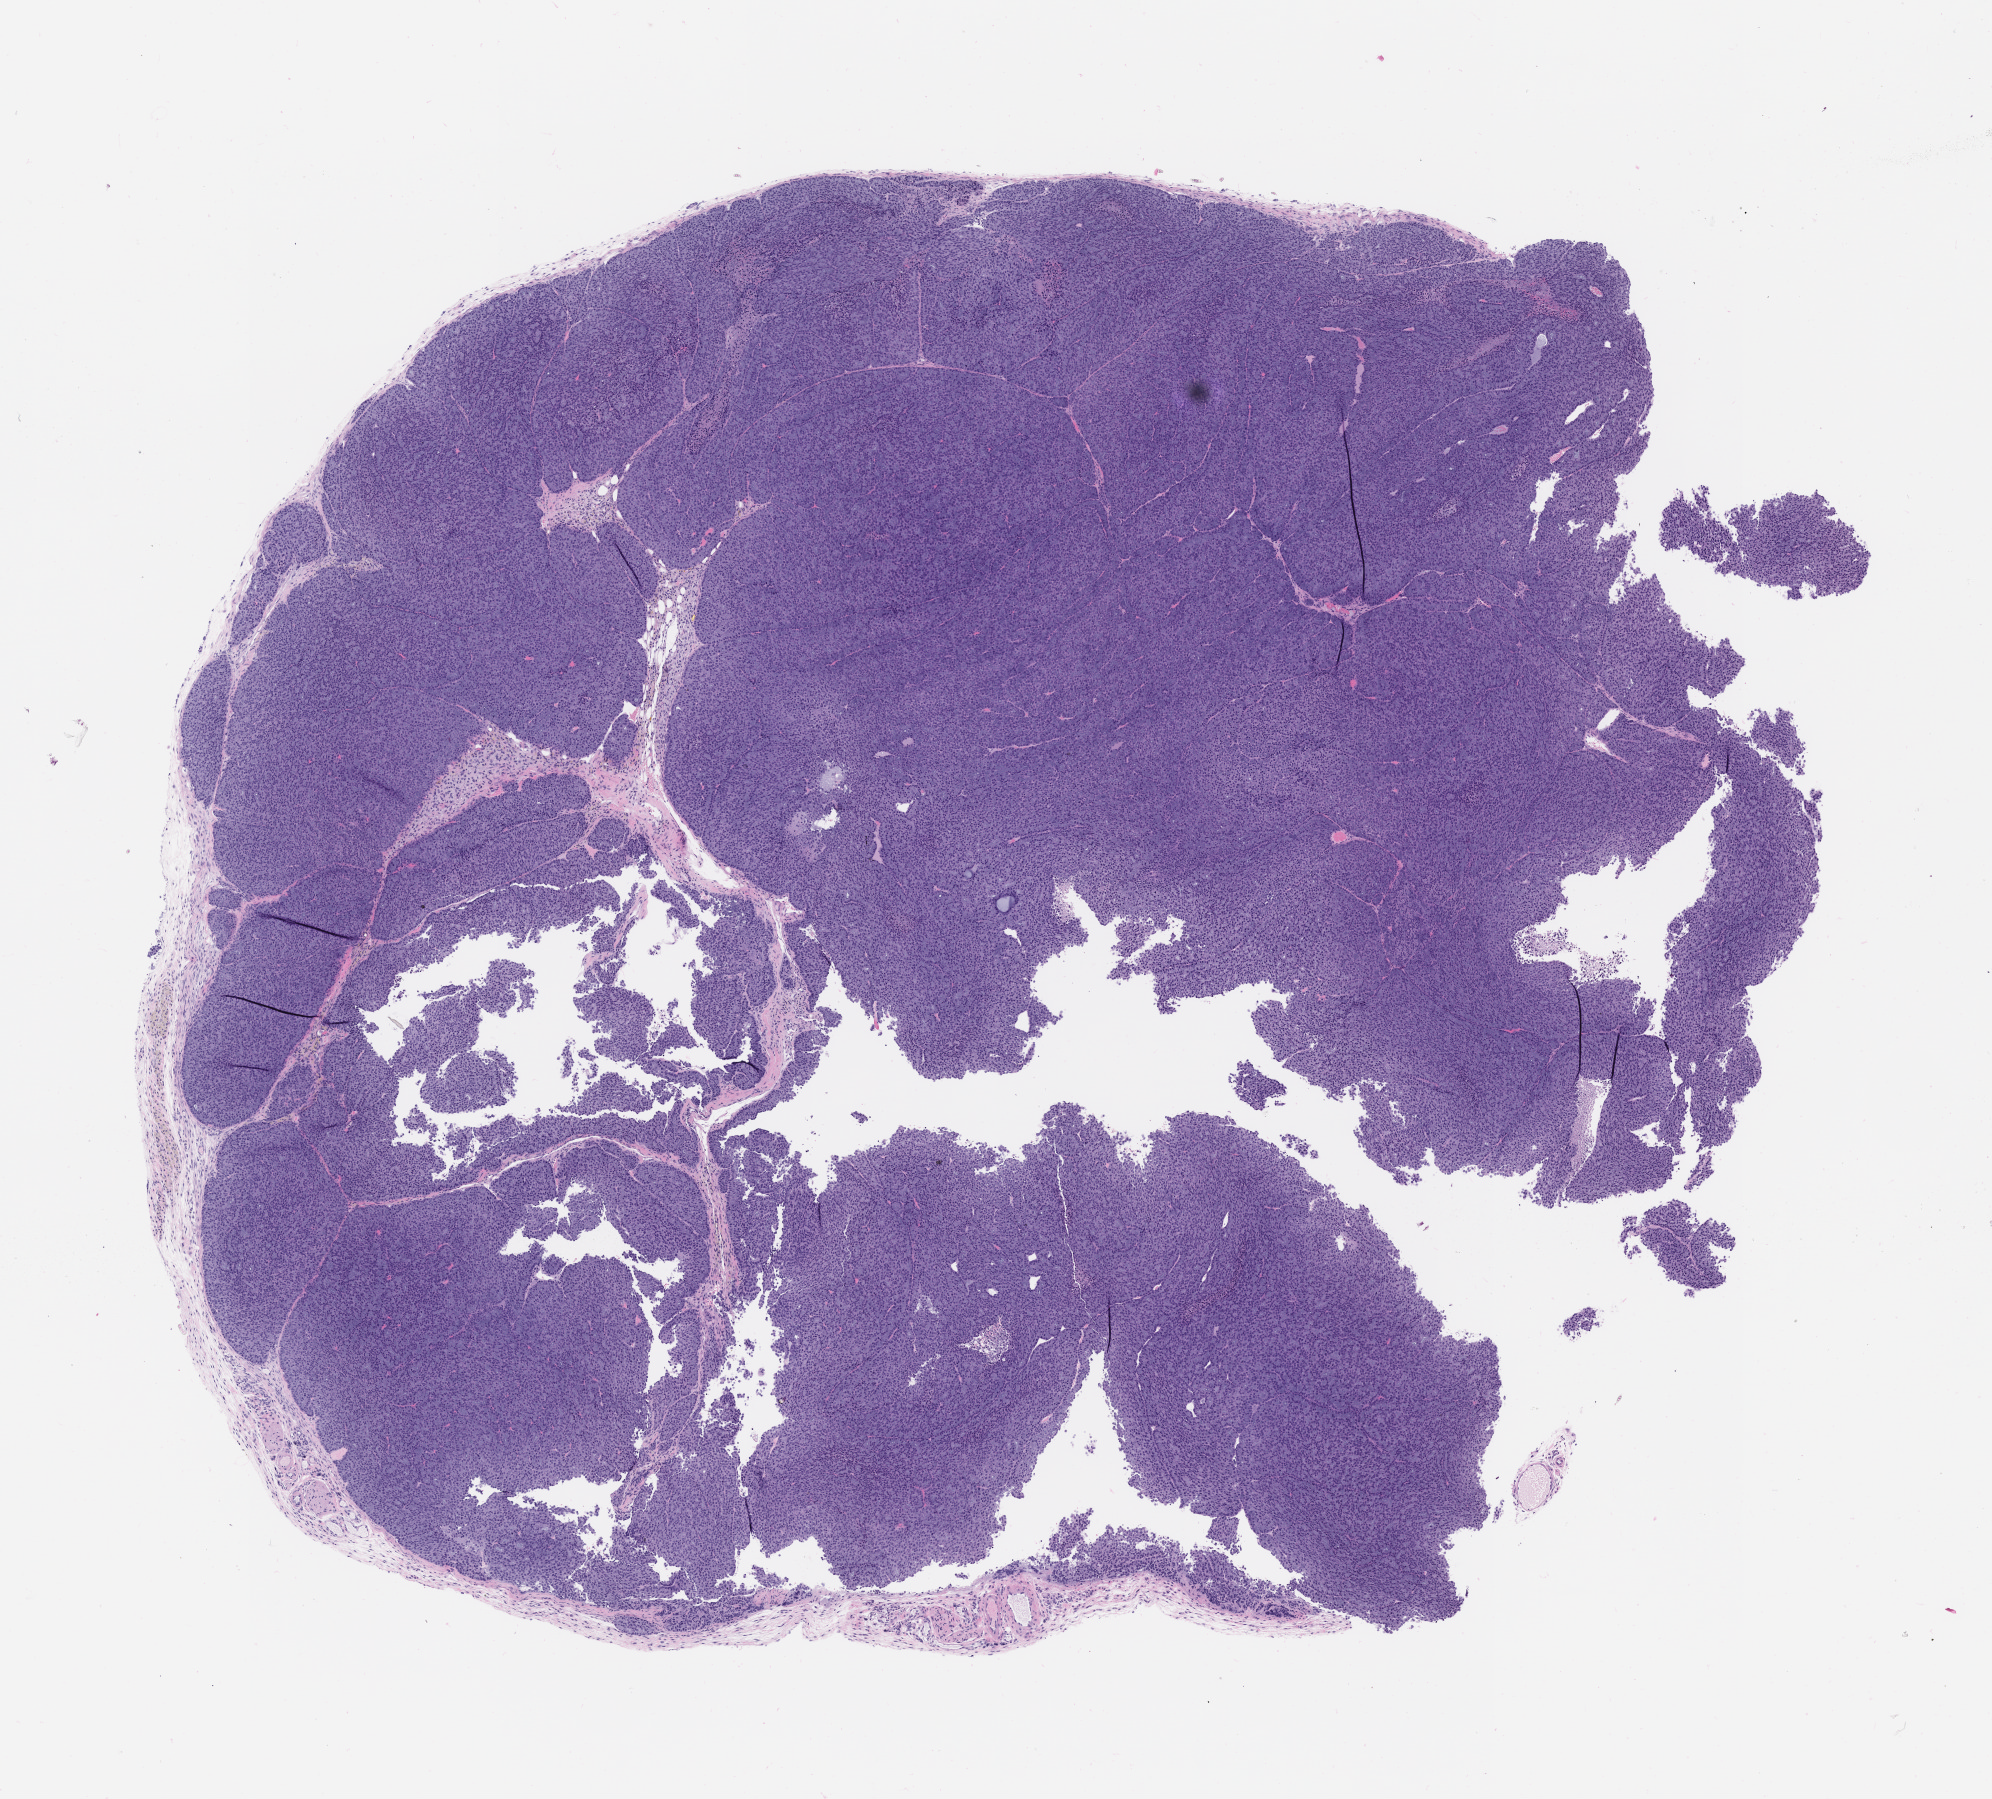
Hematoxylin and eosin (H&E) whole-slide image of a patient-derived xenograft (PDX) tumor grown in a mouse, passage 2, low-resolution overview of the scanned area, about 8.0 x 7.2 mm; formalin-fixed paraffin-embedded section; originating tumor site category: head and neck.
Originating patient diagnosis: Acinar Cell Carcinoma.